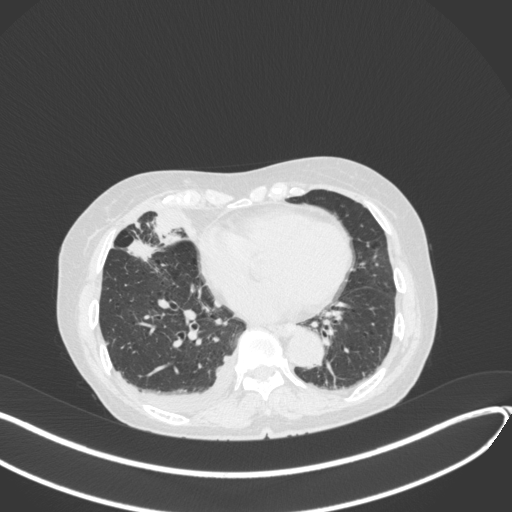
Chest CT, one axial slice; position 146 of 418 along the scan axis; lung window (W 1500 / L -600 HU); 512 × 512 image matrix, field of view 400 × 400 mm. Female patient, age 75 years. Case-level facts recorded for this patient, not image findings: clinical TNM (as recorded): T2a N3 M0.
Outlined on this slice (bounding box drawn by a radiologist):
- lung tumour (recorded histology: adenocarcinoma): bounding box <125,234,162,264> (left, top, right, bottom; pixels)